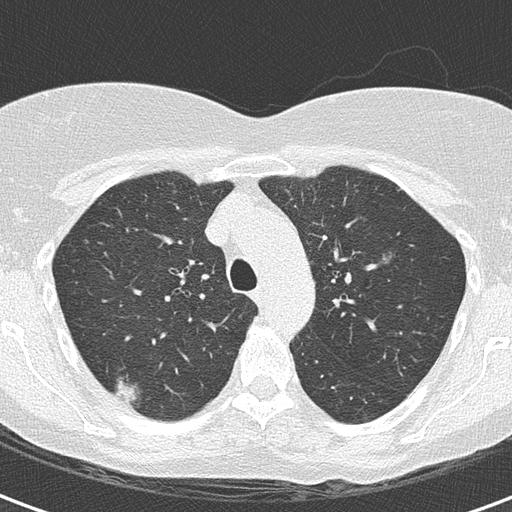
Low-dose screening chest CT, axial slice, second annual screen, lung window (W 1500 / L -600 HU), 120 kVp, slice 45 of 172 in the series, 512 × 512 image matrix. Female, age 56 years at enrolment. Current smoker at enrolment.
Expert reader's lesion annotation, bounding box (x1, y1, x2, y2) in pixels: (93, 365, 153, 415). Screening reader's record for this exam (one nodule recorded; not confirmed to be the boxed lesion): non-calcified nodule or mass ≥4 mm, right upper lobe, 18 × 18 mm, mixed attenuation, pre-existing on the prior screen: yes. Official screen result: positive, other. Participant outcome: lung cancer diagnosed 93 days after this screen — bronchiolo-alveolar adenocarcinoma, NOS, right upper lobe, well differentiated (G1), stage IA (AJCC 6th edition), 15 mm at pathology.